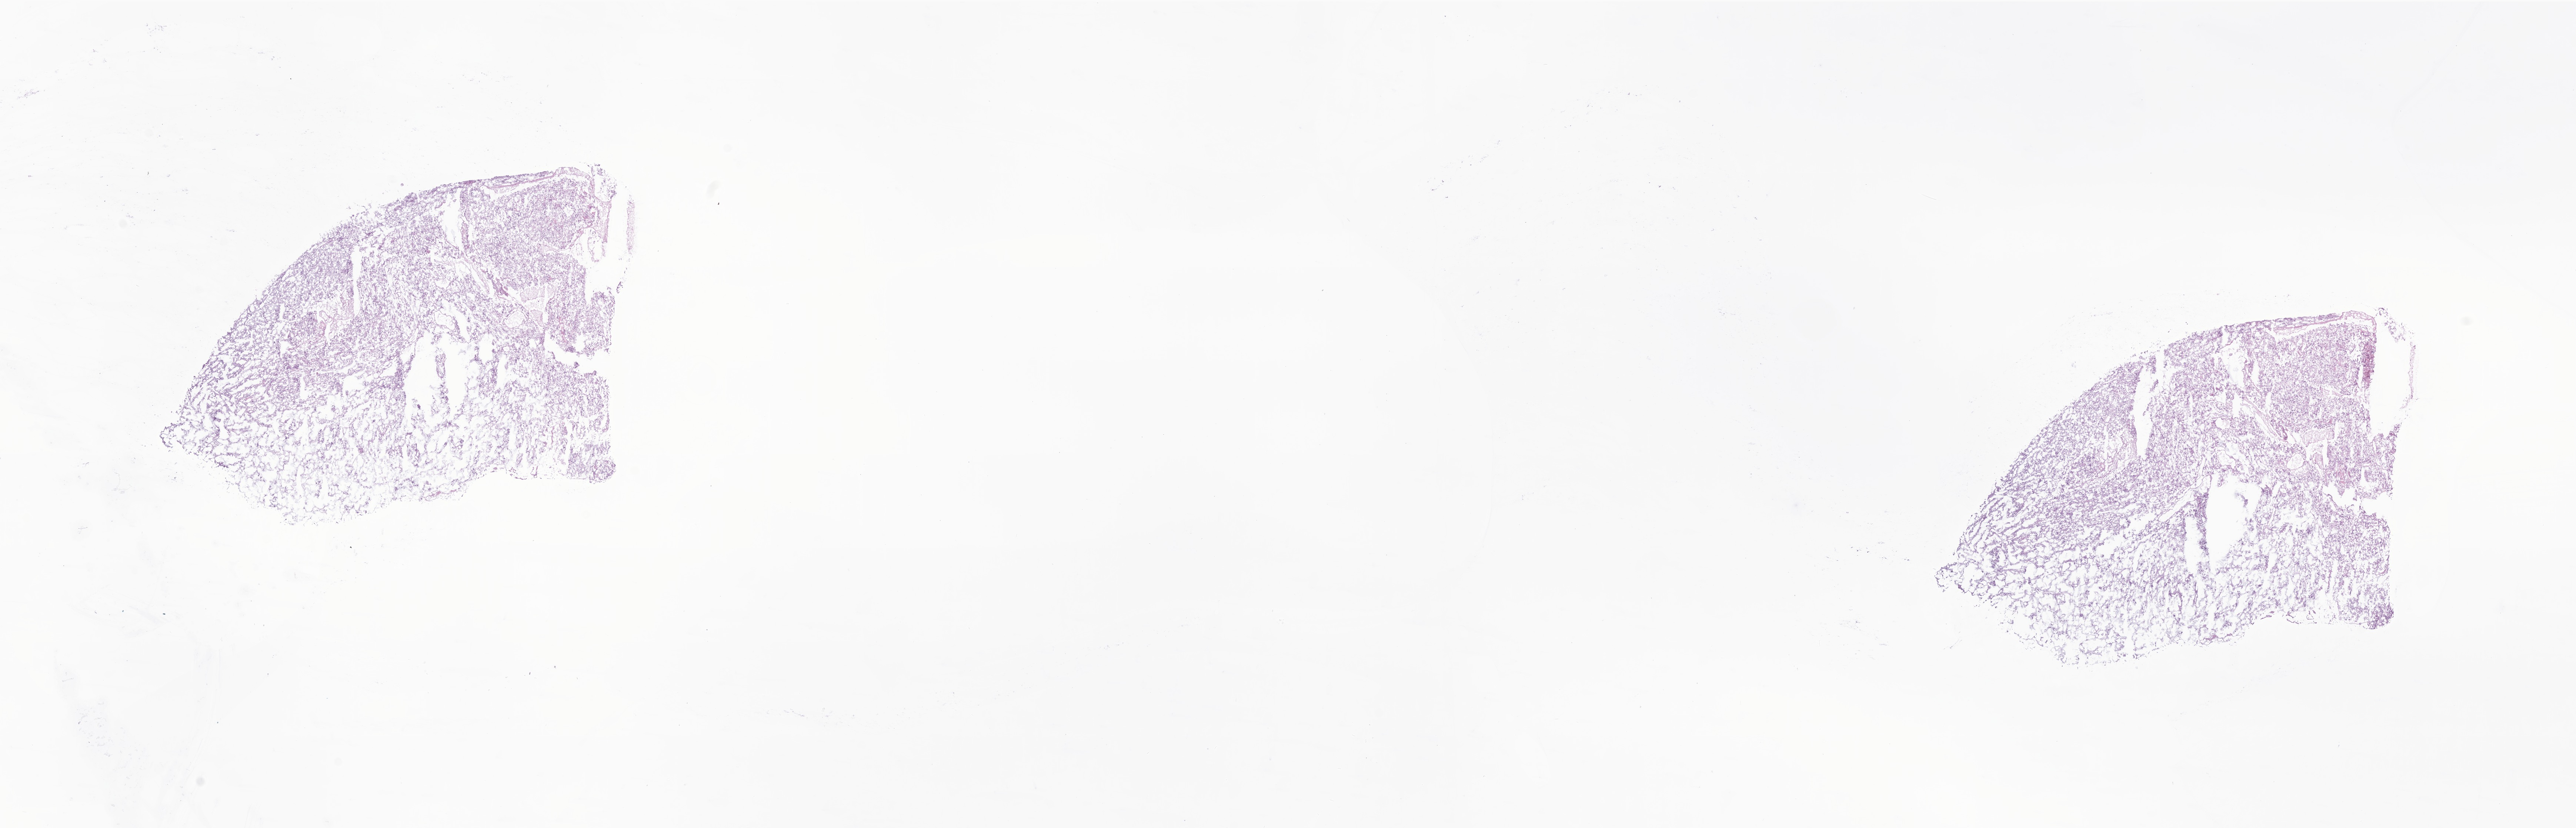
Whole-slide image, H&E stain of tumor tissue from the brain — whole scanned area (about 29.3 x 9.4 mm) shown as a low-resolution overview, cryosection (OCT / tissue freezing medium). Male patient, age 112 months.
Recorded diagnosis: Glioma, malignant.